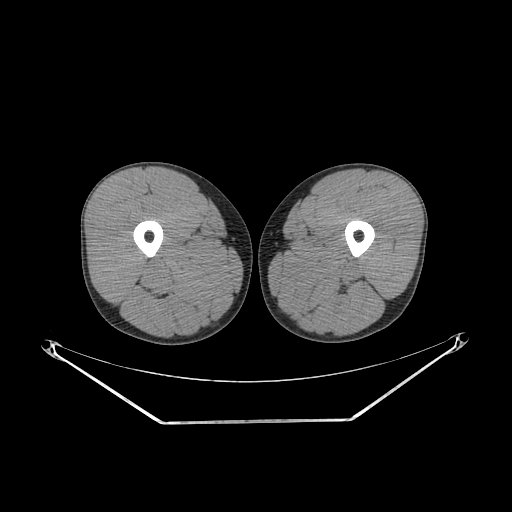
CT of an extremity soft-tissue mass (from a PET/CT study), one axial slice; position 229 of 267 along the scan axis; 140 kVp; soft-tissue window (W 400 / L 40 HU); 512 × 512 image matrix, field of view 500 × 500 mm. Male patient. From the clinical record (not read from this slice): histological type: extraskeletal osteosarcoma; grade: high; site of the primary tumour: left adductur.
Structures marked on this image (expert contour drawn on MRI and transferred to this co-registered scan by the dataset authors):
- gross tumour volume (mass): bounding box <270,246,369,312> (left, top, right, bottom; pixels)